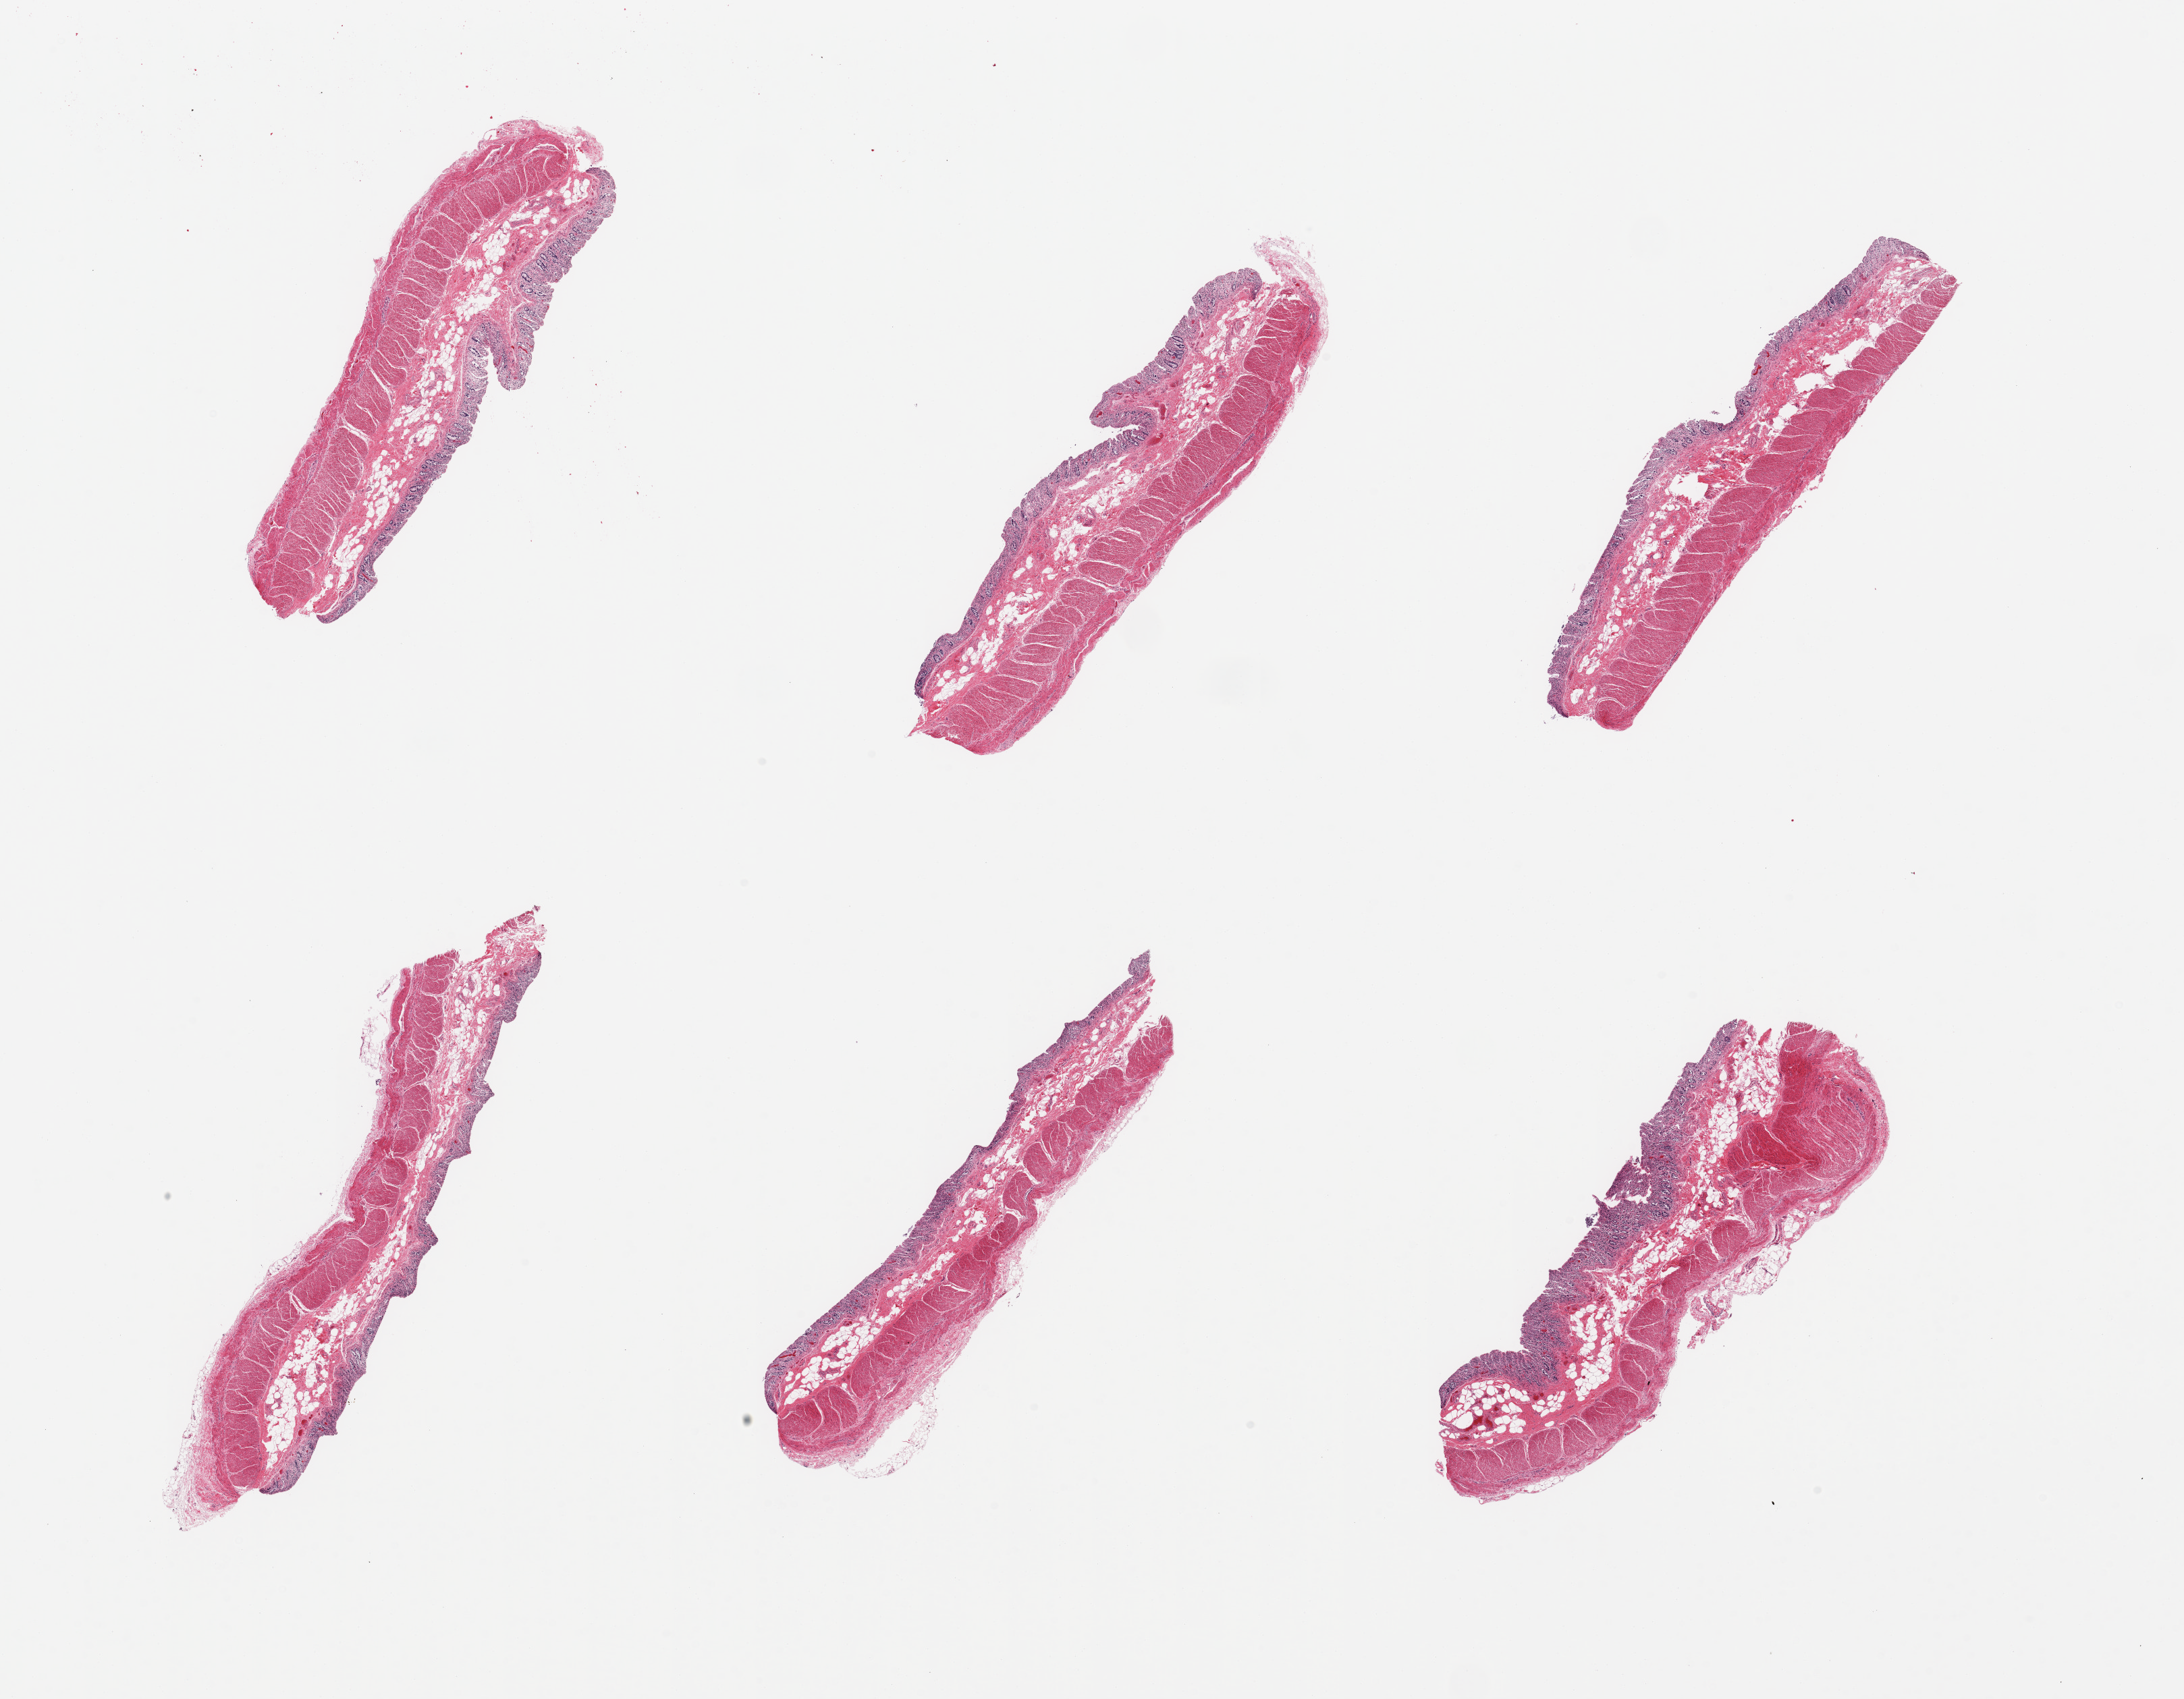
Digitized hematoxylin and eosin (H&E)-stained section, shown as a low-resolution overview of the whole scanned area (about 25.6 x 19.9 mm, slide scanned at 20x), PAXgene-fixed, paraffin-embedded tissue, sampled site (target tissue): transverse colon, tissue donor sample. Female donor.
Pathologist's review note for this sample: 6 pieces; mucosa largely autolyzed; muscularis intact.